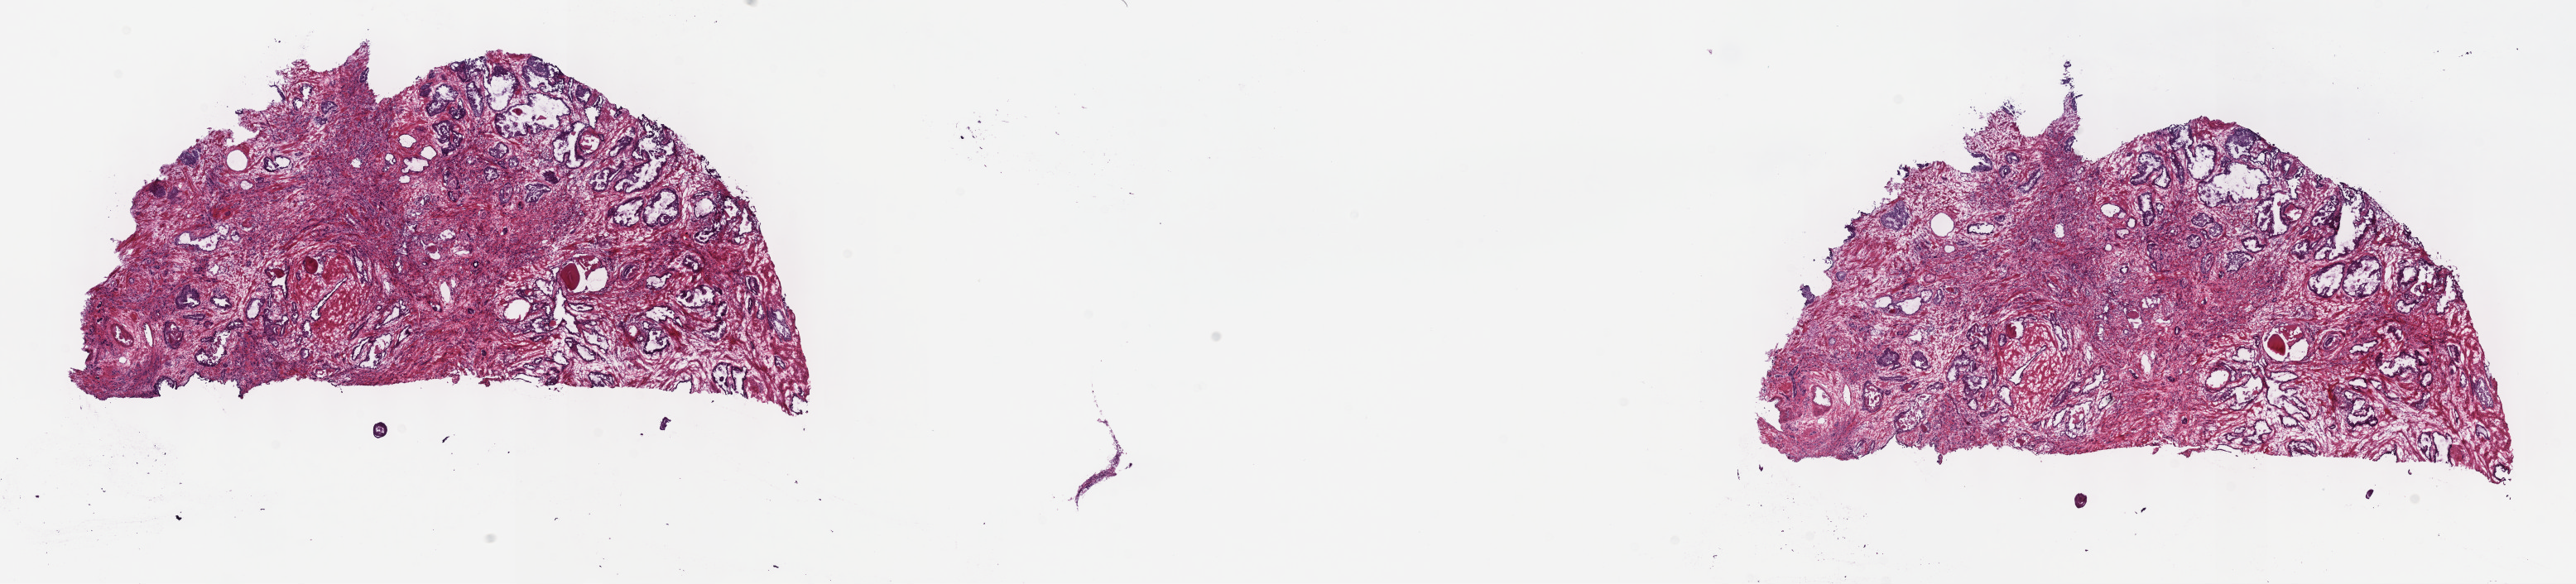
Digitized H&E-stained tissue section (whole slide), shown as a low-resolution overview of the whole scanned area (about 25.2 x 5.7 mm), frozen section from the top of the tissue portion, prostate, primary tumour sample. Male patient; age at initial diagnosis 59 years.
Histologic diagnosis: Infiltrating duct carcinoma, NOS (prostate gland).